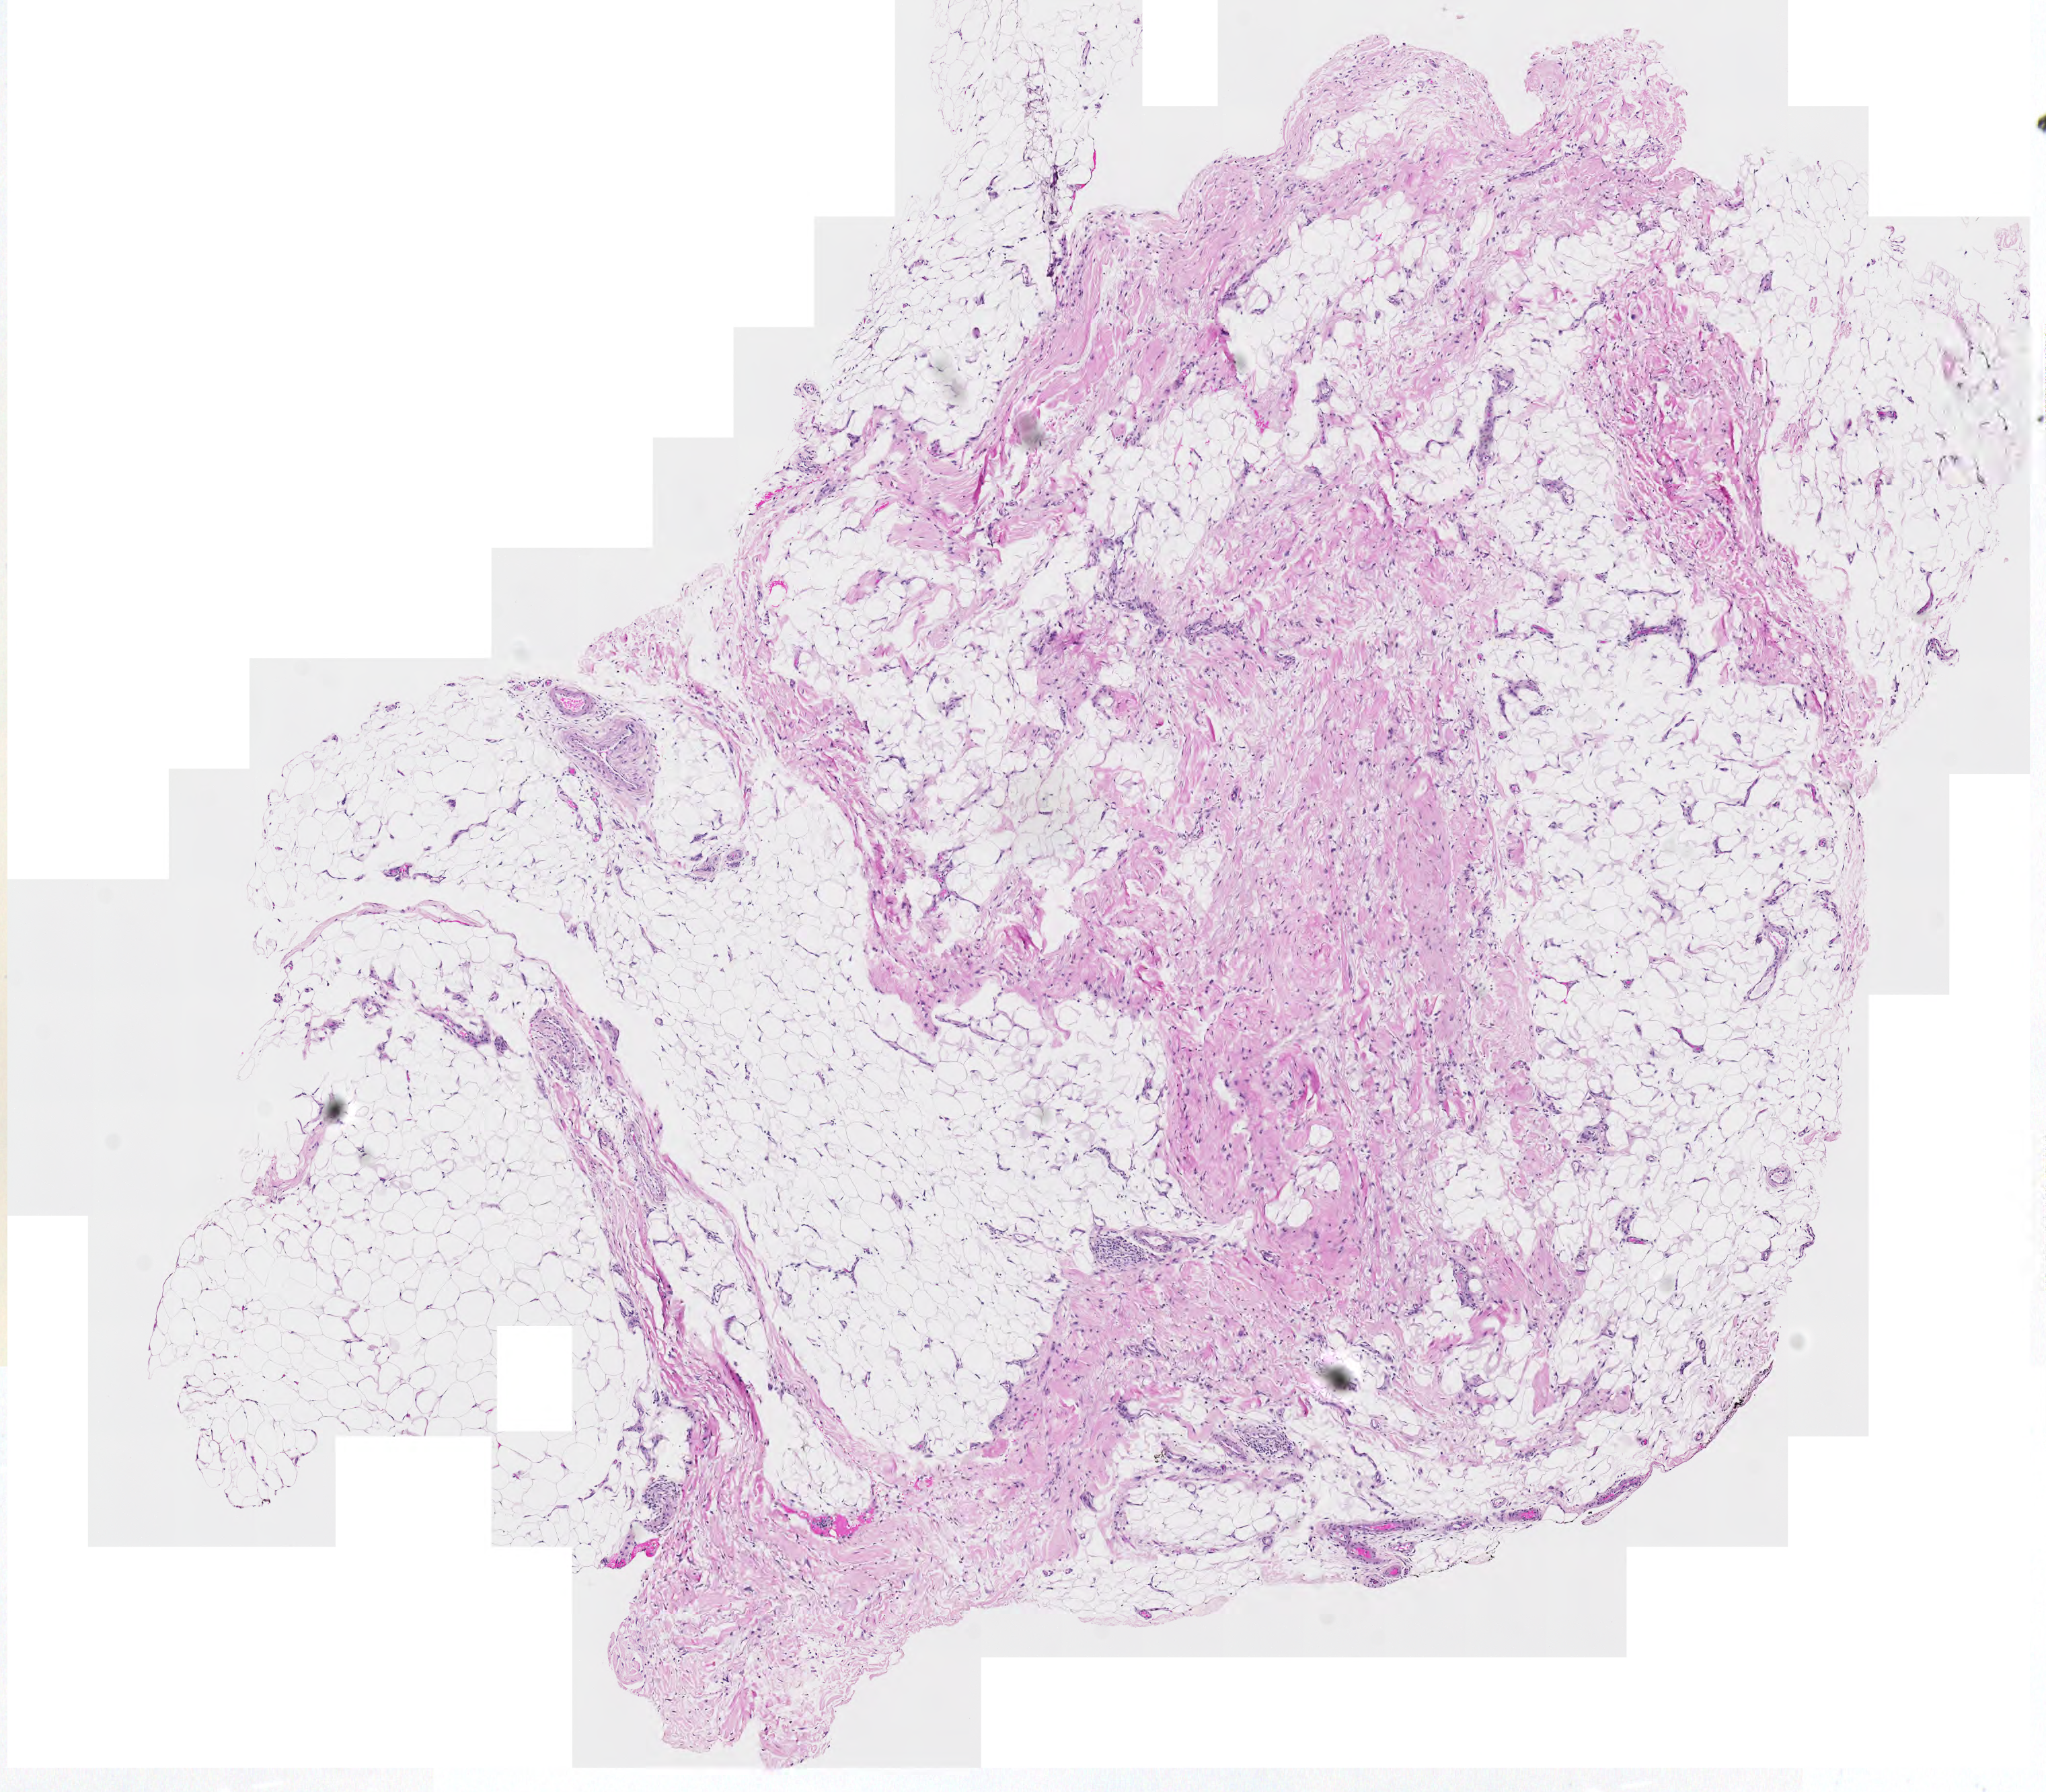
Hematoxylin and eosin (H&E) stained whole-slide image — a low-resolution overview of the entire scanned area, about 7.9 x 6.9 mm (slide scanned at 20x); normal (non-tumour) tissue sample. Patient: male, age 81 years.
- this section: normal (non-tumour) tissue from the same patient
- patient diagnosis (cohort enrolment): sarcoma (site not recorded at cohort level)